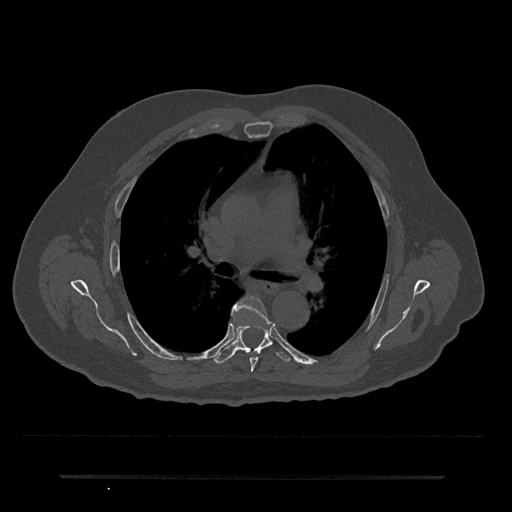
CT including the spine, one axial slice; position 457 of 797 along the scan axis; bone window (W 1800 / L 400 HU); 512 × 512 image matrix. Male patient, age 69 years. From the clinical record (not read from this slice): primary cancer: prostate.
Outlined on this slice (semi-automatic segmentation, software-assisted and operator-edited):
- T5 vertebra: bounding box (x1, y1, x2, y2) in pixels: (232, 296, 269, 372)
- T6 vertebra: (214, 317, 290, 364)